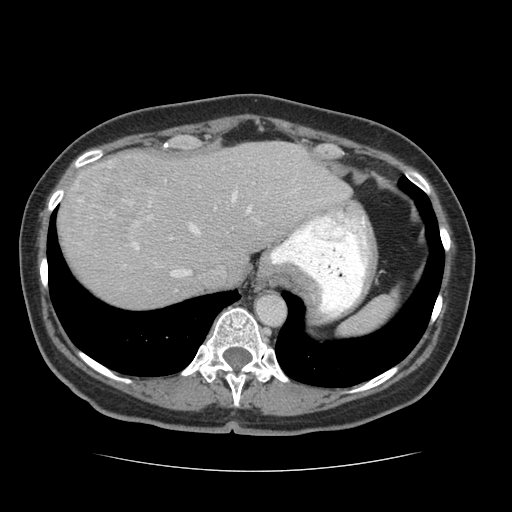
Contrast-enhanced abdominal CT (liver protocol), one axial slice. Slice 55 of 75 in the series (ordered by position). 140 kVp. Soft-tissue window (W 400 / L 40 HU). 2.5 mm slice thickness. 512 × 512 image matrix. From the clinical record (not read from this slice): diagnosis: hepatocellular carcinoma (patient treated with transarterial chemoembolisation; whether this scan precedes or follows treatment is not stated here); TNM stage (as recorded): Stage-I; Child-Pugh class: A; tumour differentiation: moderately differentiated.
Structures marked on this image (semi-automatic segmentation, software-assisted and operator-edited):
- abdominal aorta: bounding box (x1, y1, x2, y2) in pixels: (257, 295, 285, 326)
- liver parenchyma outside the tumour (the mass and vessels are separate outlines, so this box may not span the whole liver): (58, 142, 350, 308)
- mass: (71, 153, 171, 247)
- liver vessels: (132, 183, 321, 278)